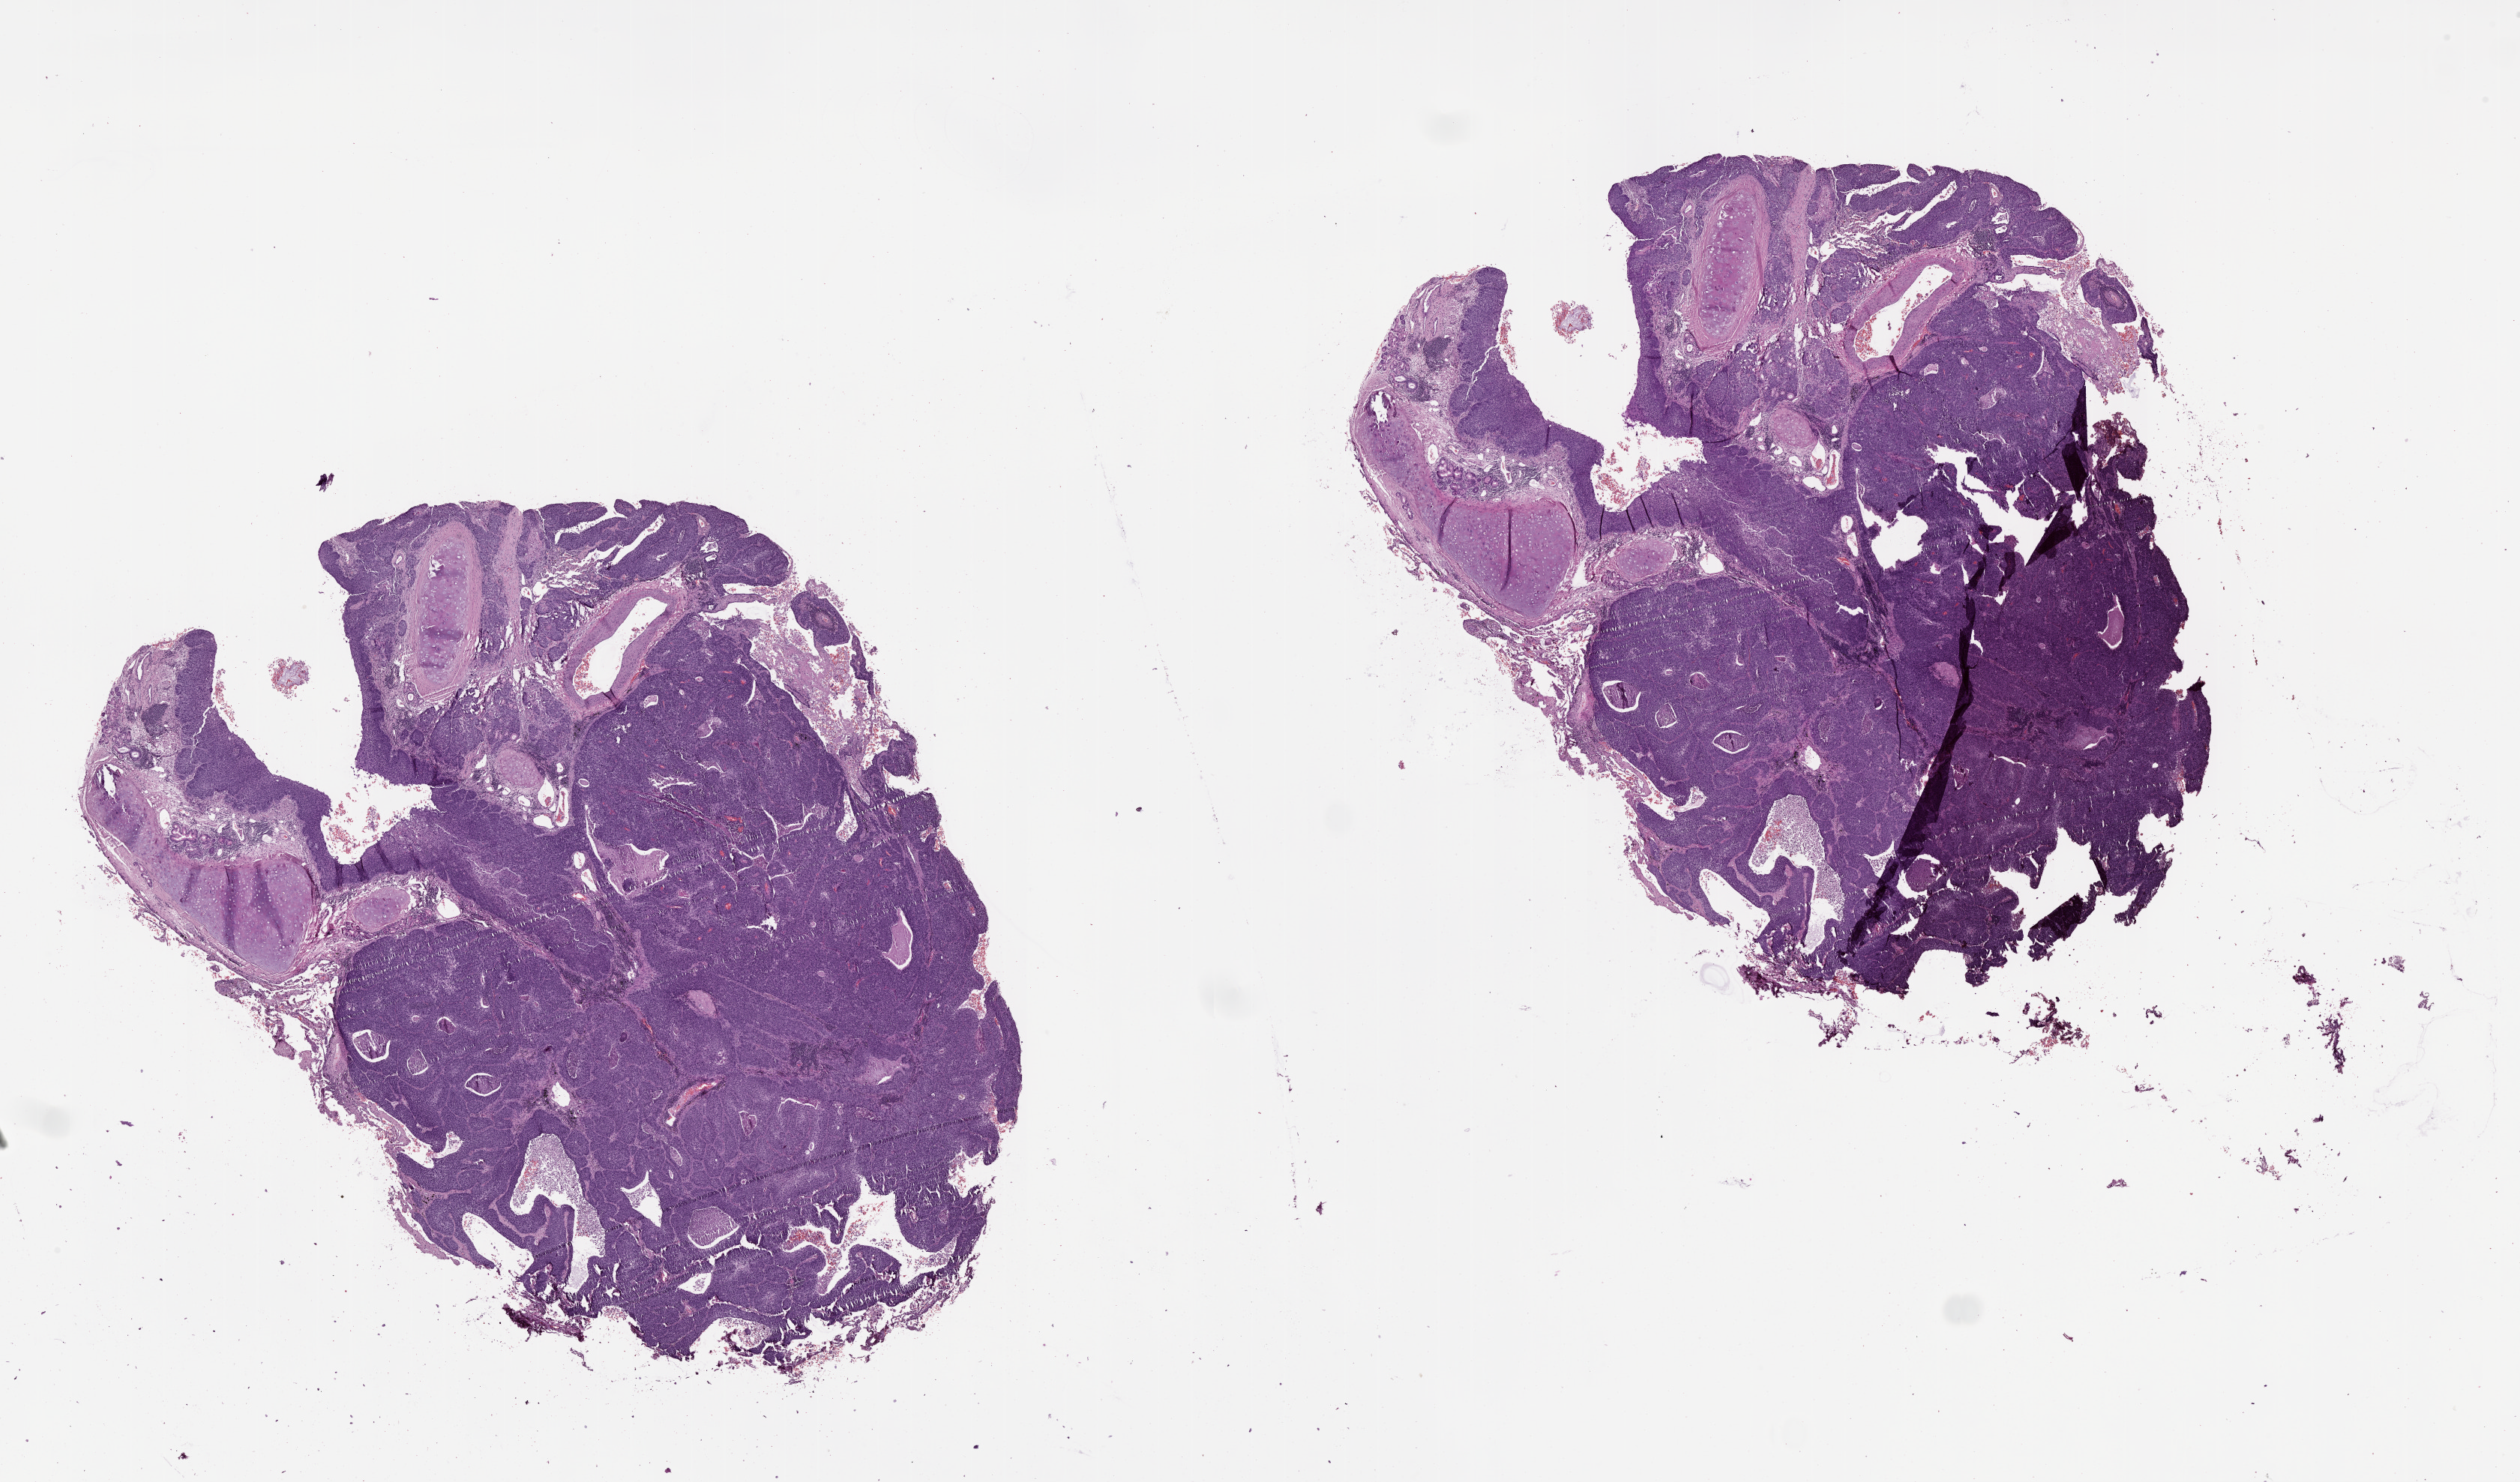
Whole-slide histology image, H&E-stained — a low-resolution overview of the entire scanned area, about 27.1 x 15.9 mm; lung, tumour tissue. 67-year-old male patient.
Patient diagnosis (cohort enrolment): squamous cell carcinoma (lung).